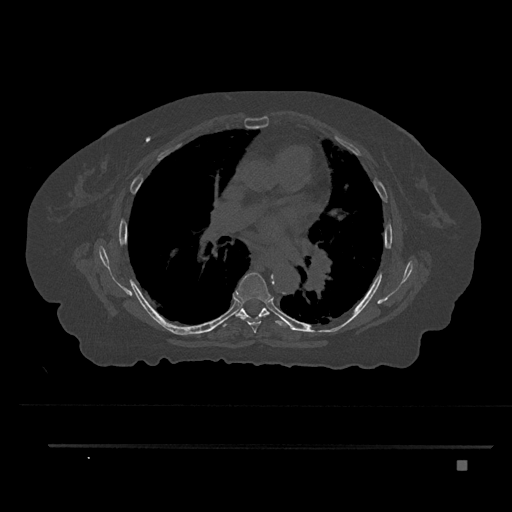
CT including the spine, one axial slice. Position 510 of 797 along the scan axis. Reconstruction kernel Br40s/3. Bone window (W 1800 / L 400 HU). 0.5 mm slice thickness. 512 × 512 image matrix, field of view 437 × 437 mm. Patient: female, 76 years. Case-level facts recorded for this patient, not image findings: primary cancer: lung.
Structures marked on this image (semi-automatically segmented with operator editing):
- T6 vertebra: bounding box (x1, y1, x2, y2) in pixels: (234, 272, 271, 333)
- T7 vertebra: (223, 308, 289, 327)